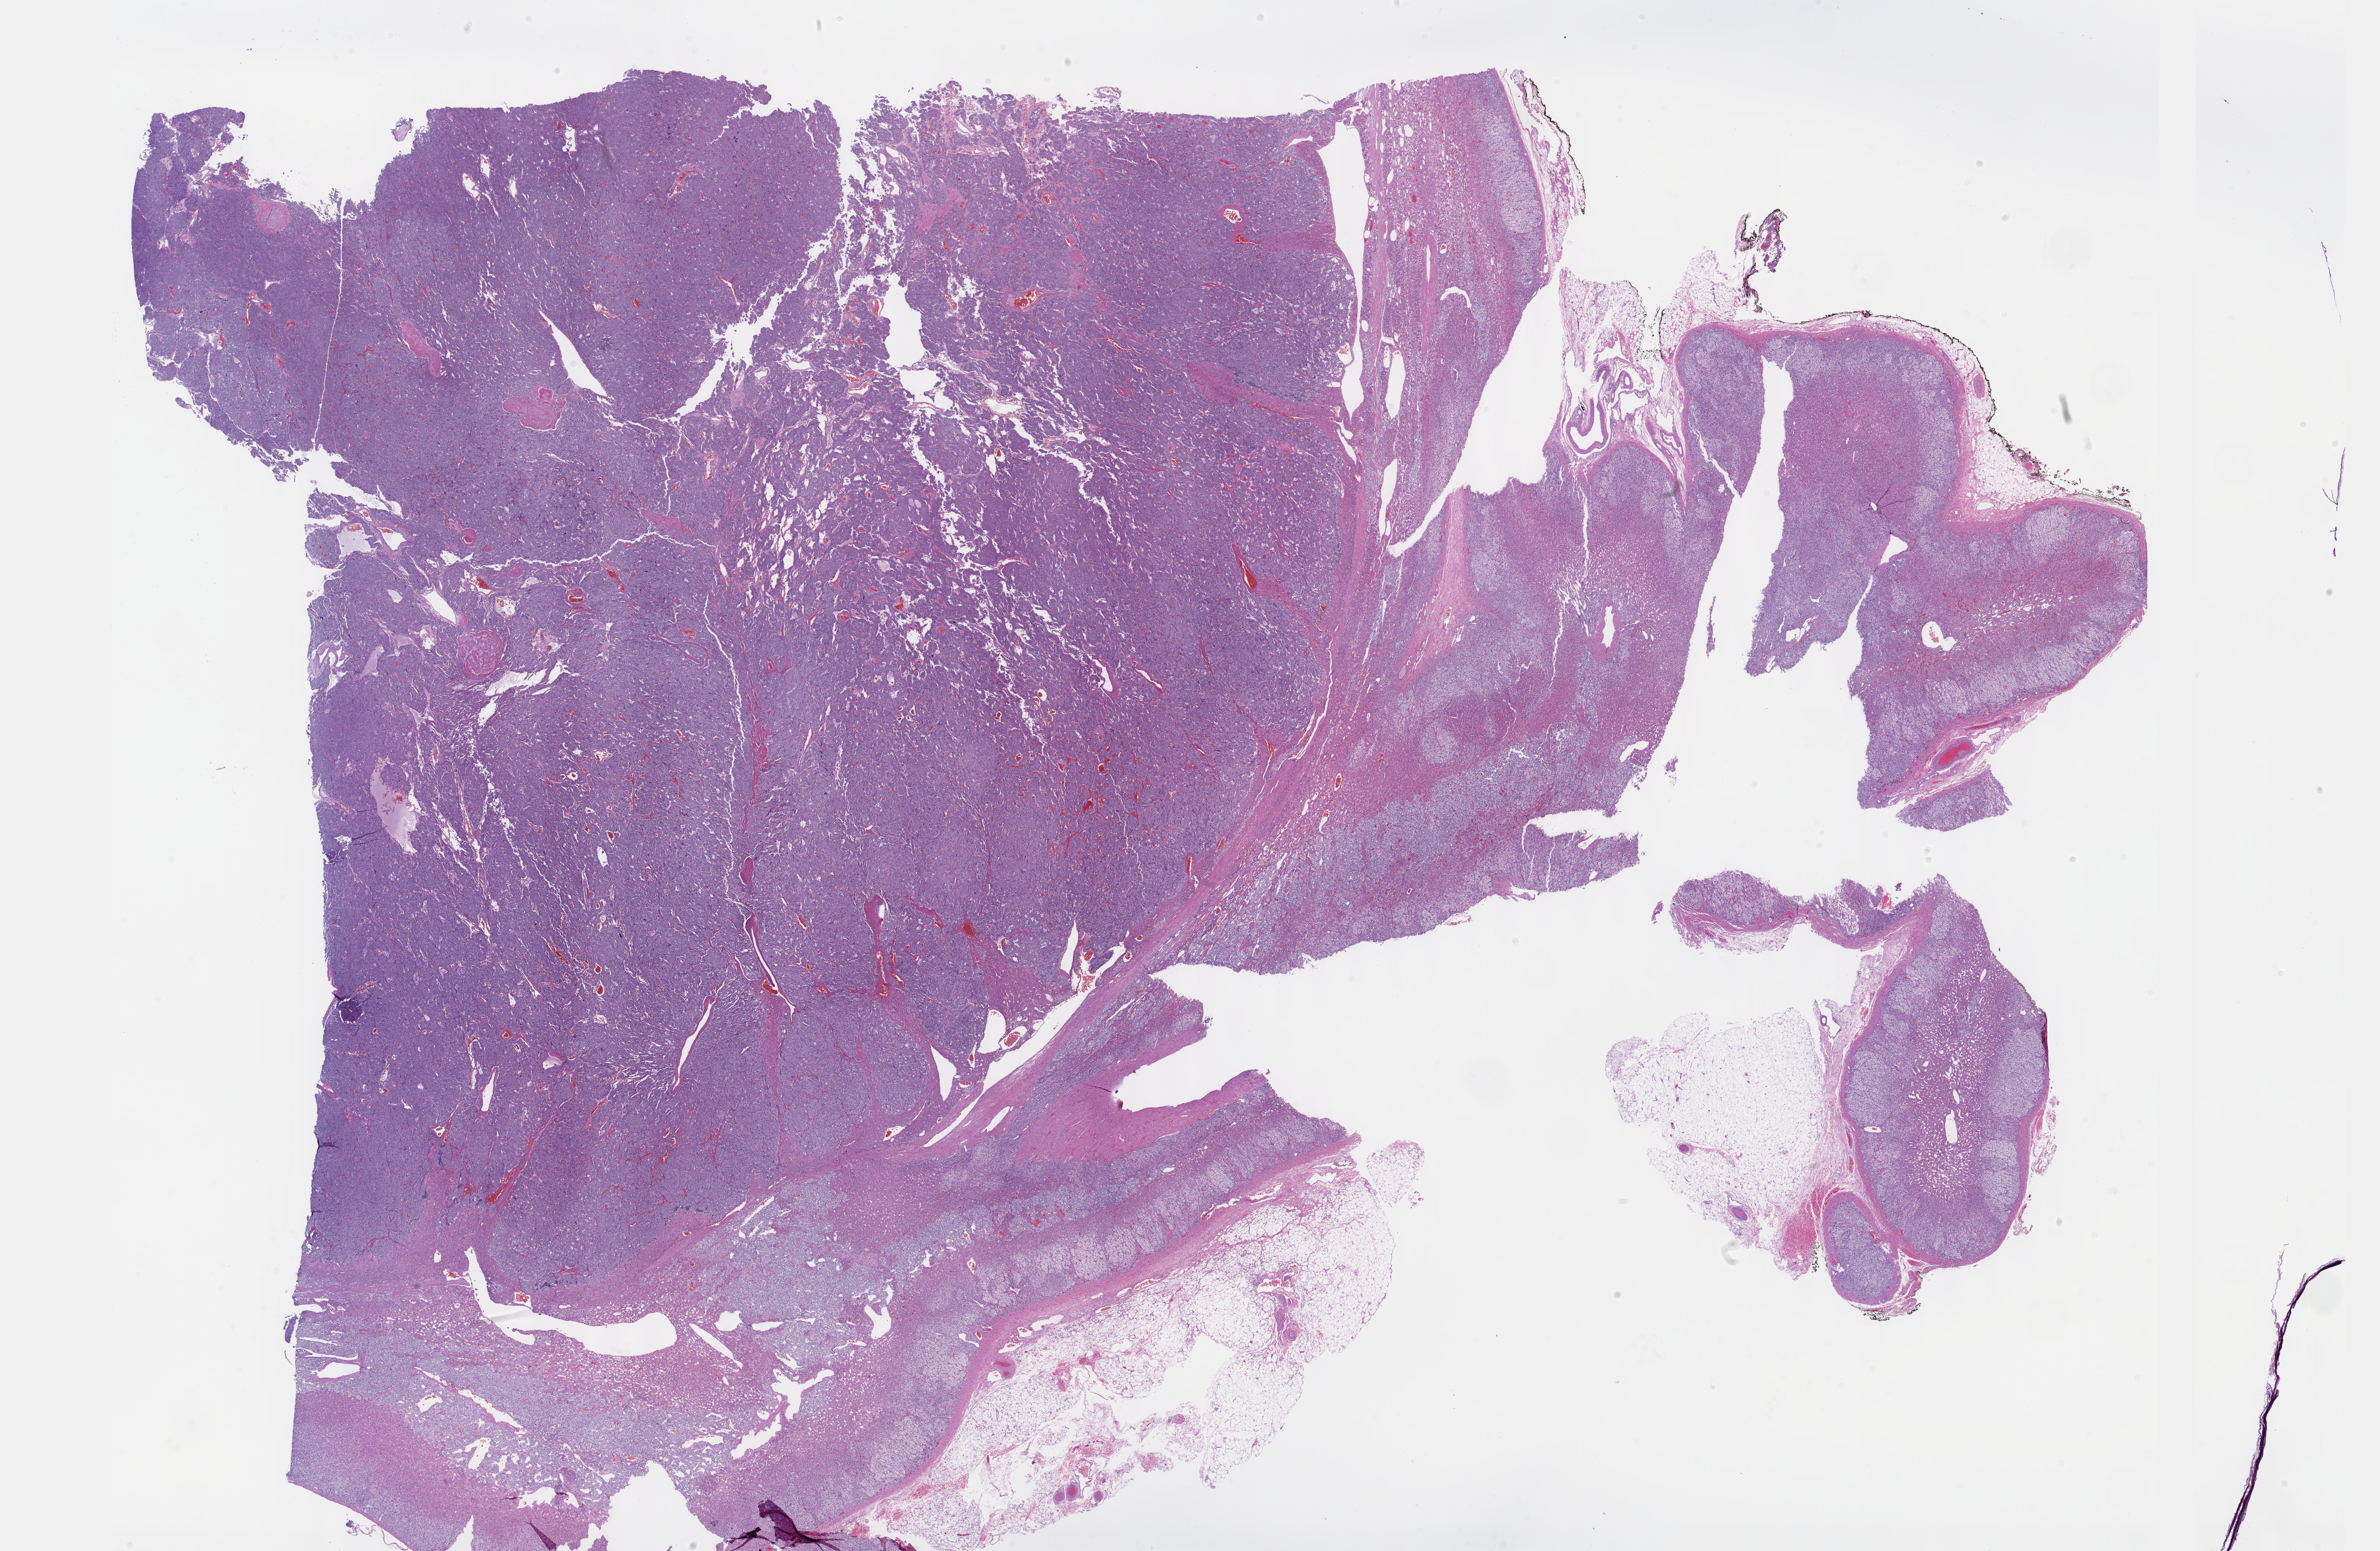
Digitized H&E tissue section (whole slide) — whole scanned area (about 32.2 x 21.0 mm) shown as a low-resolution overview, formalin-fixed paraffin-embedded (FFPE) diagnostic section, sample: primary tumour, adrenal gland. Male, age 36 years at initial diagnosis.
* histologic diagnosis: Pheochromocytoma, NOS